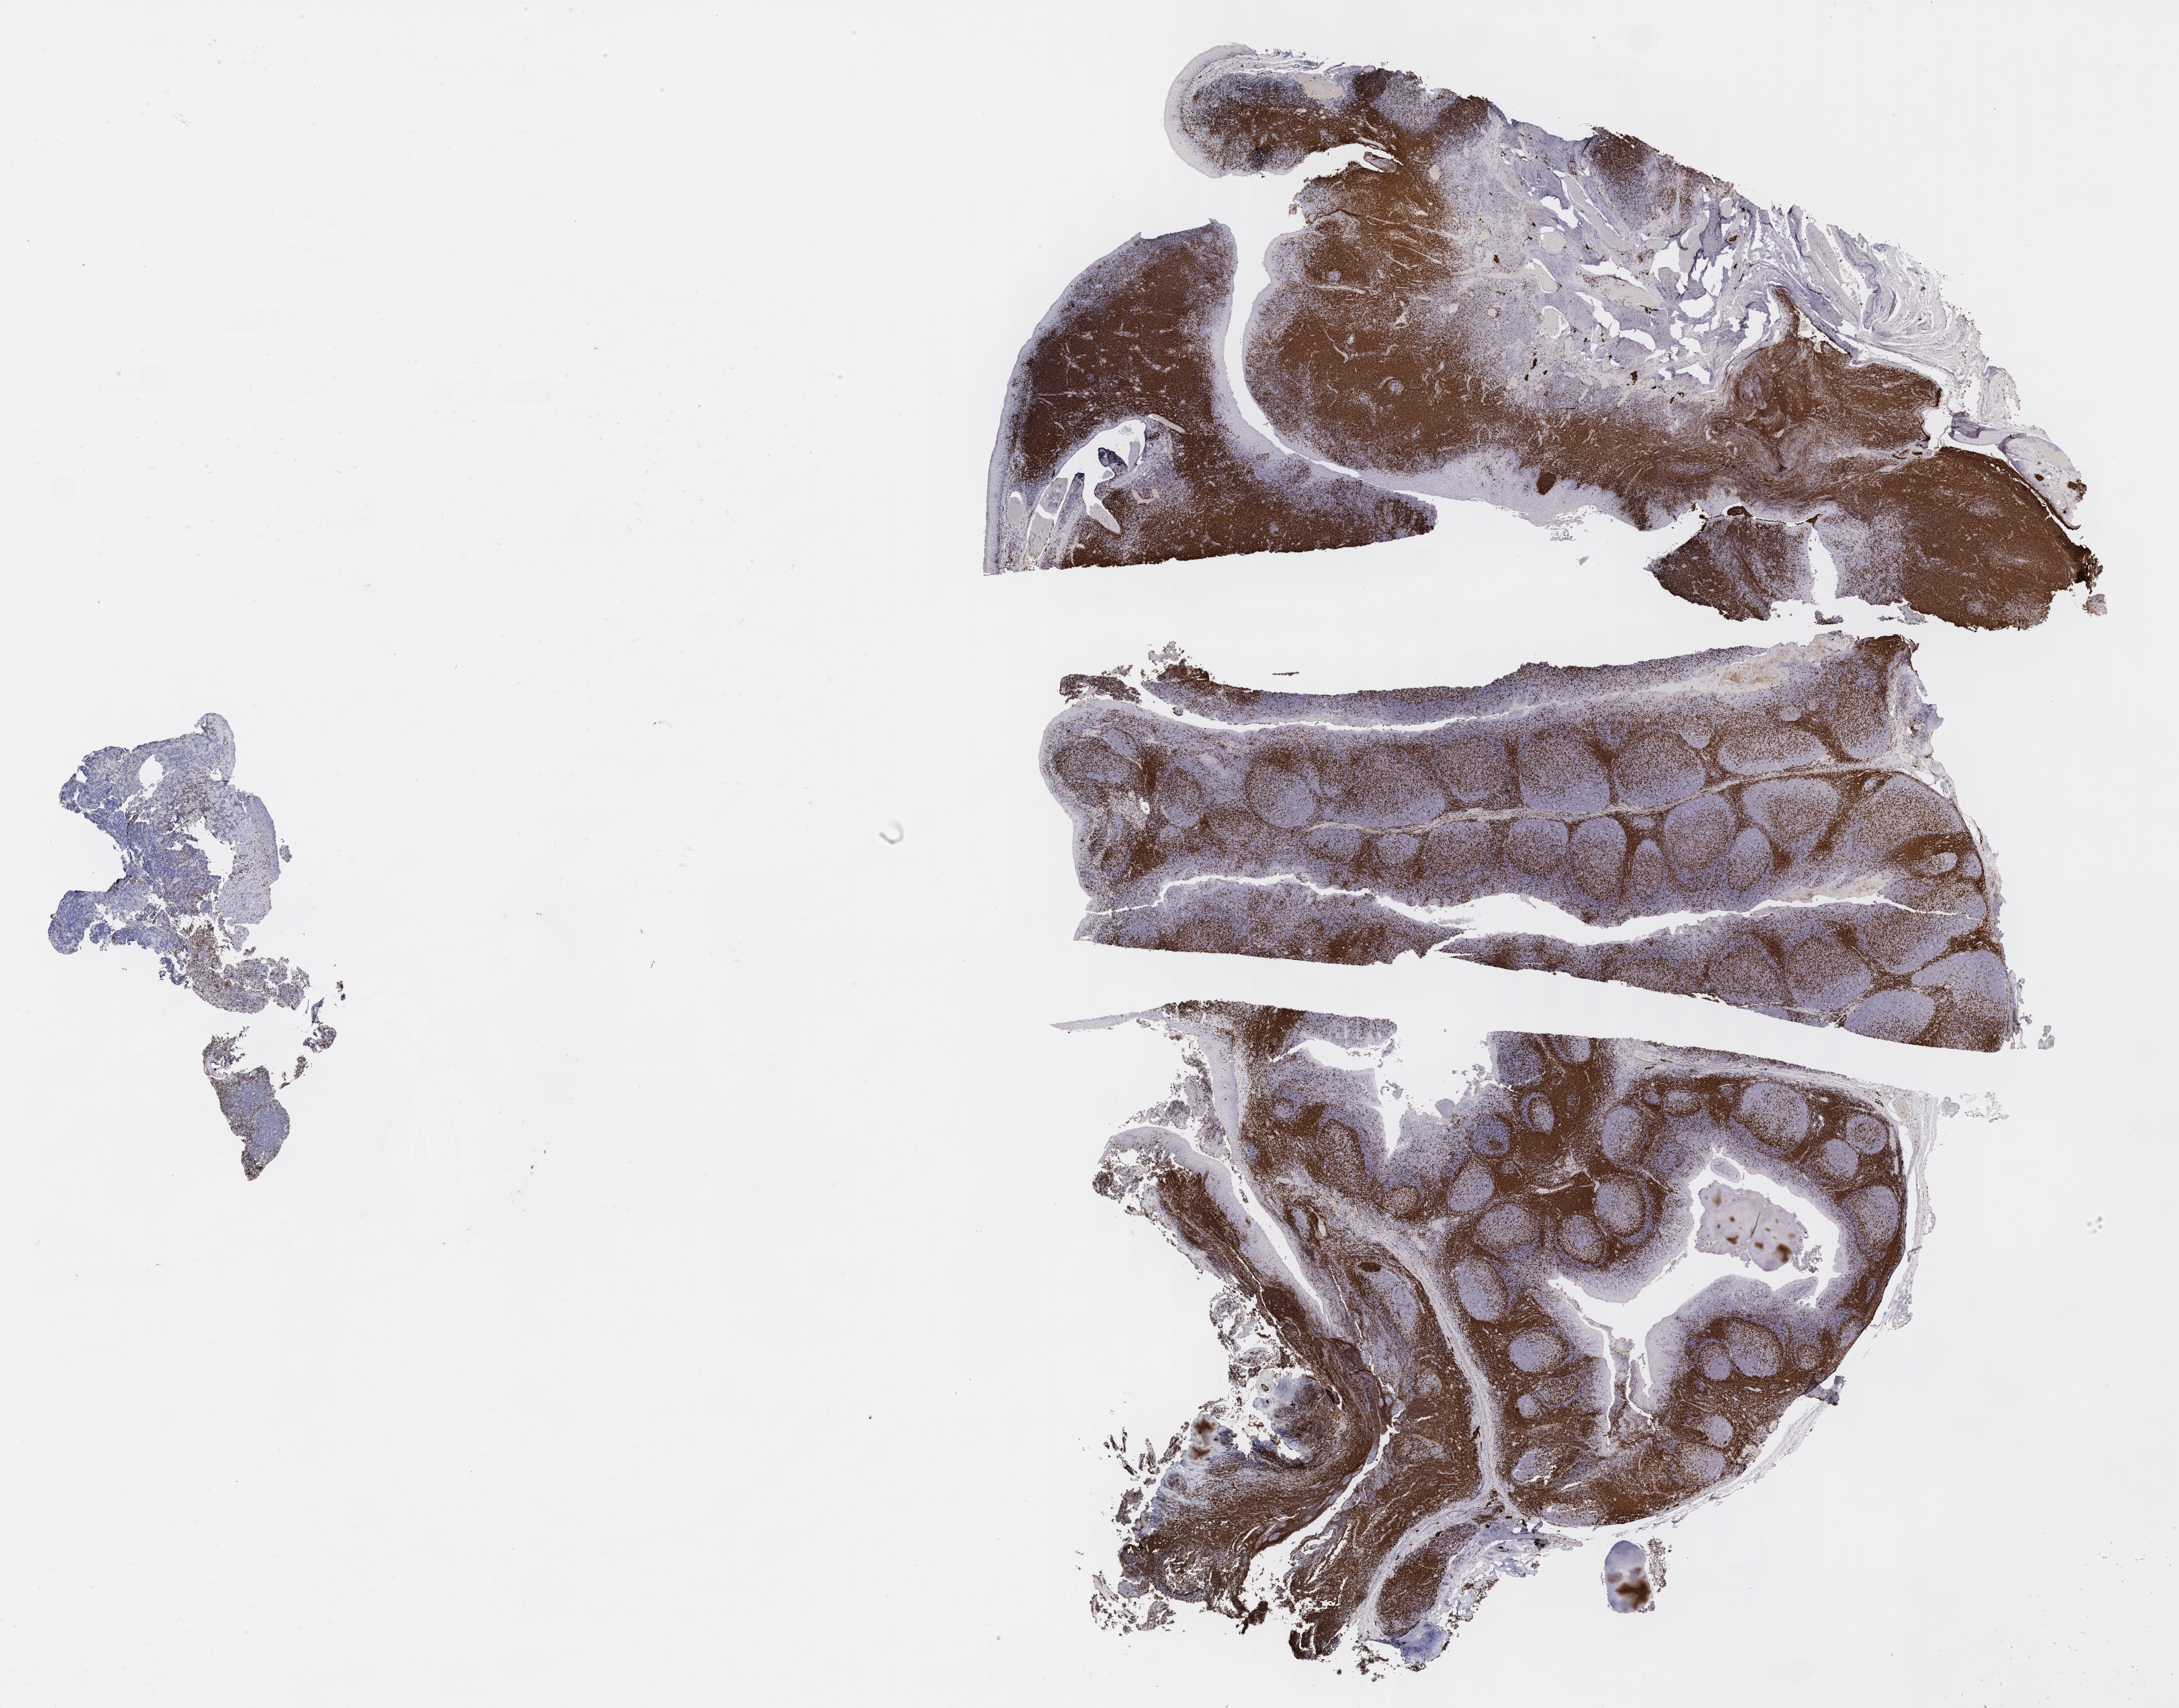
IHC for CD3, whole-slide image — low-resolution overview of the scanned area, about 27.2 x 21.3 mm, specimen: tumor tissue, anatomic site: gum of mandible. Patient male; age 10 years.
Diagnosis: Burkitt lymphoma, NOS.